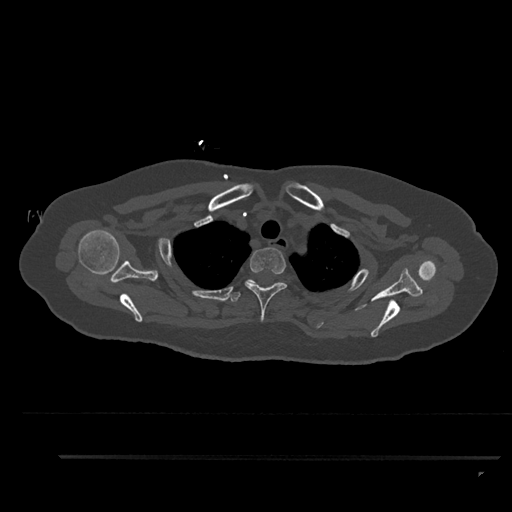
CT including the spine, one axial slice; reconstruction kernel Br40s/3; 120 kVp; bone window (W 1800 / L 400 HU); 0.5 mm slice thickness; 512 × 512 image matrix, field of view 408 × 408 mm. Patient: female, 44 years. From the clinical record (not read from this slice): primary cancer: renal; vertebrae with lytic lesions (as recorded): L1.
Outlined on this slice (semi-automatic segmentation, software-assisted and operator-edited):
- T1 vertebra: bounding box <272,284,274,286> (left, top, right, bottom; pixels)
- T2 vertebra: <245,248,287,322>
- T3 vertebra: <228,279,255,302>